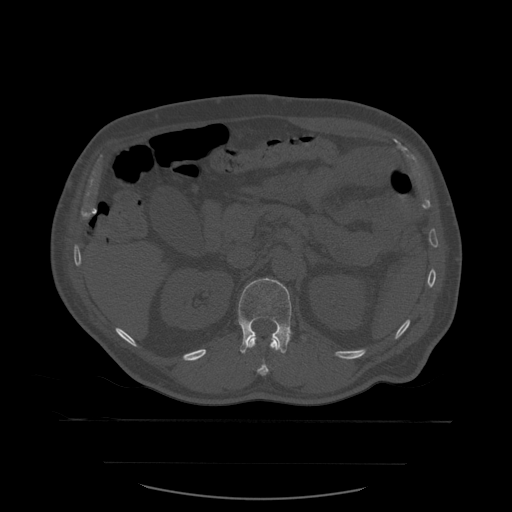
CT including the spine, one axial slice; bone window (W 1800 / L 400 HU); 1.25 mm slice thickness; 512 × 512 image matrix. Patient age 71 years. From the clinical record (not read from this slice): primary cancer: lung; vertebrae with lytic lesions (as recorded): T1, T2, L5, S1.
Structures marked on this image (semi-automatically segmented with operator editing):
- L1 vertebra: box from (x=238, y=278) to (x=292, y=352) px
- T12 vertebra: (x=241, y=334)–(x=286, y=376)